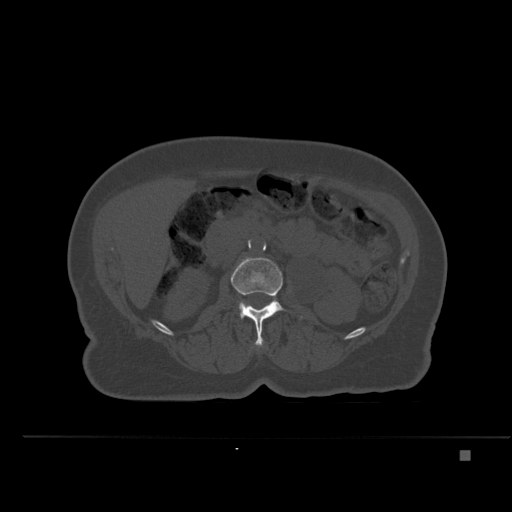
CT including the spine, one axial slice. Bone window (W 1800 / L 400 HU). 1.5 mm slice thickness. 512 × 512 image matrix, field of view 422 × 422 mm. Patient: female, 74 years. Case-level facts recorded for this patient, not image findings: primary cancer: colon.
Outlined on this slice (semi-automatic segmentation, software-assisted and operator-edited):
- L2 vertebra: bounding box <231,257,302,346> (left, top, right, bottom; pixels)